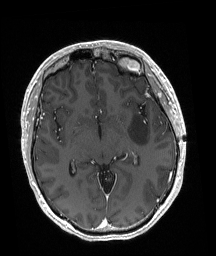
Brain MRI from a brain-tumour surgery series, one axial slice; position 108 of 192 along the scan axis; T1-weighted post-contrast; 216 × 256 image matrix, field of view 211 × 250 mm. Case-level facts recorded for this patient, not image findings: histopathology: Astrocytoma; WHO grade: 3; IDH mutation: yes; tumour location: Left Posterior Frontal.
Annotated regions visible in this slice (outlined manually by an expert reader):
- tumour: bounding box (x1, y1, x2, y2) in pixels: (129, 113, 149, 145)